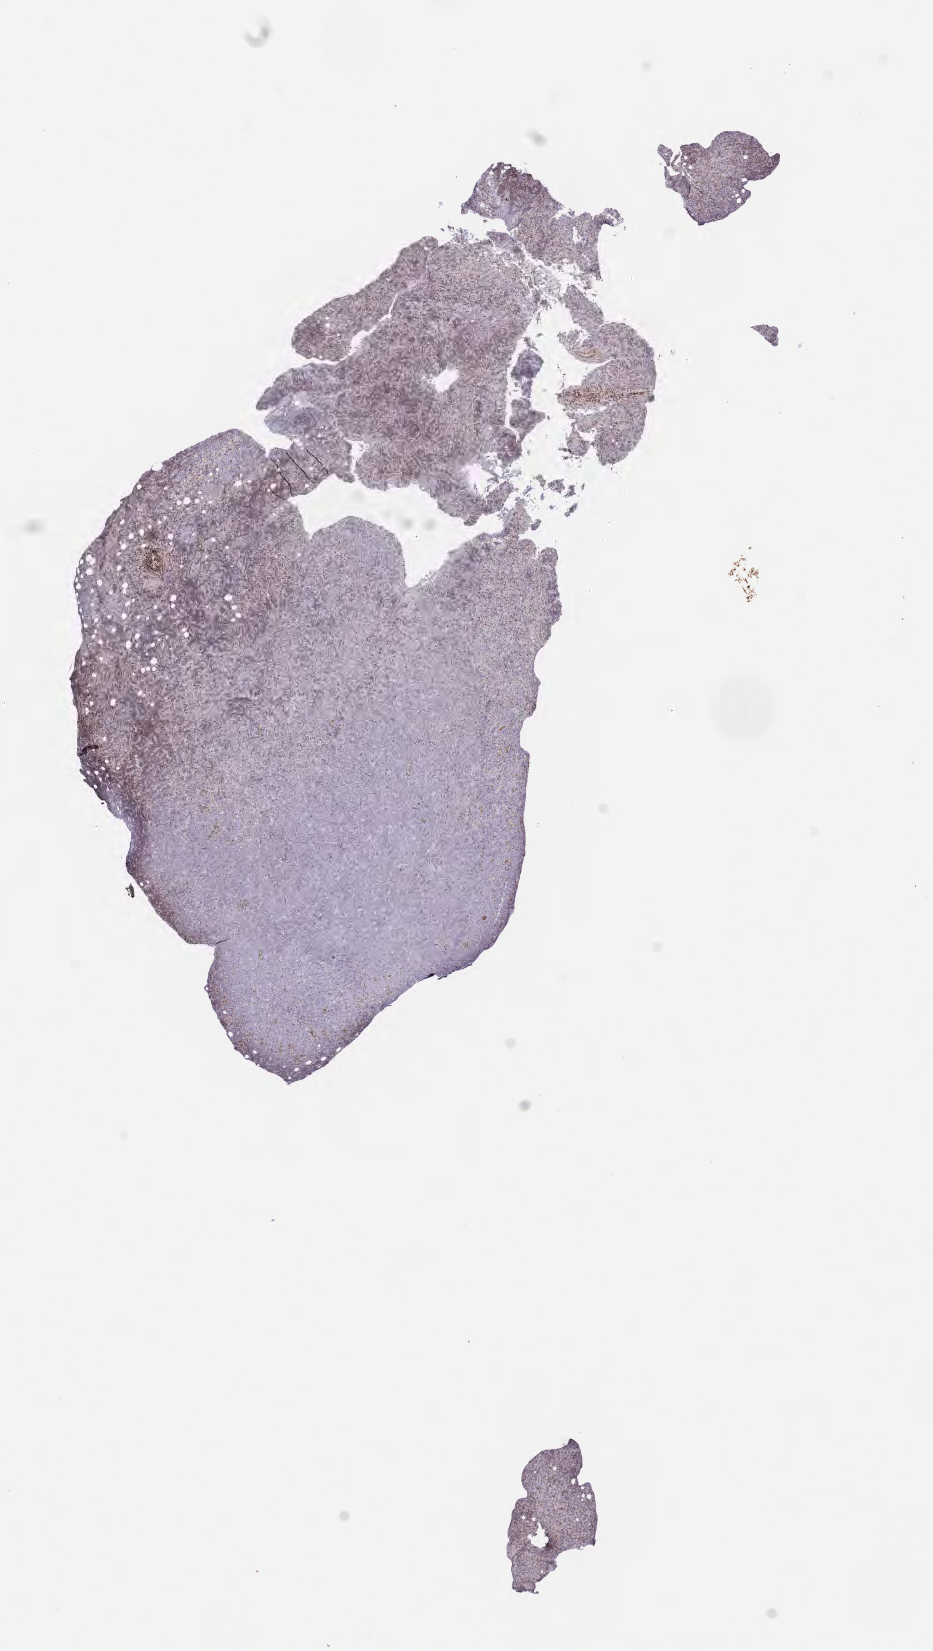
IHC for BCL2, whole-slide image — low-resolution overview of the scanned area, about 7.5 x 13.4 mm. Tumor tissue. Patient female; 40 years old.
Diagnosis: Burkitt lymphoma, NOS.